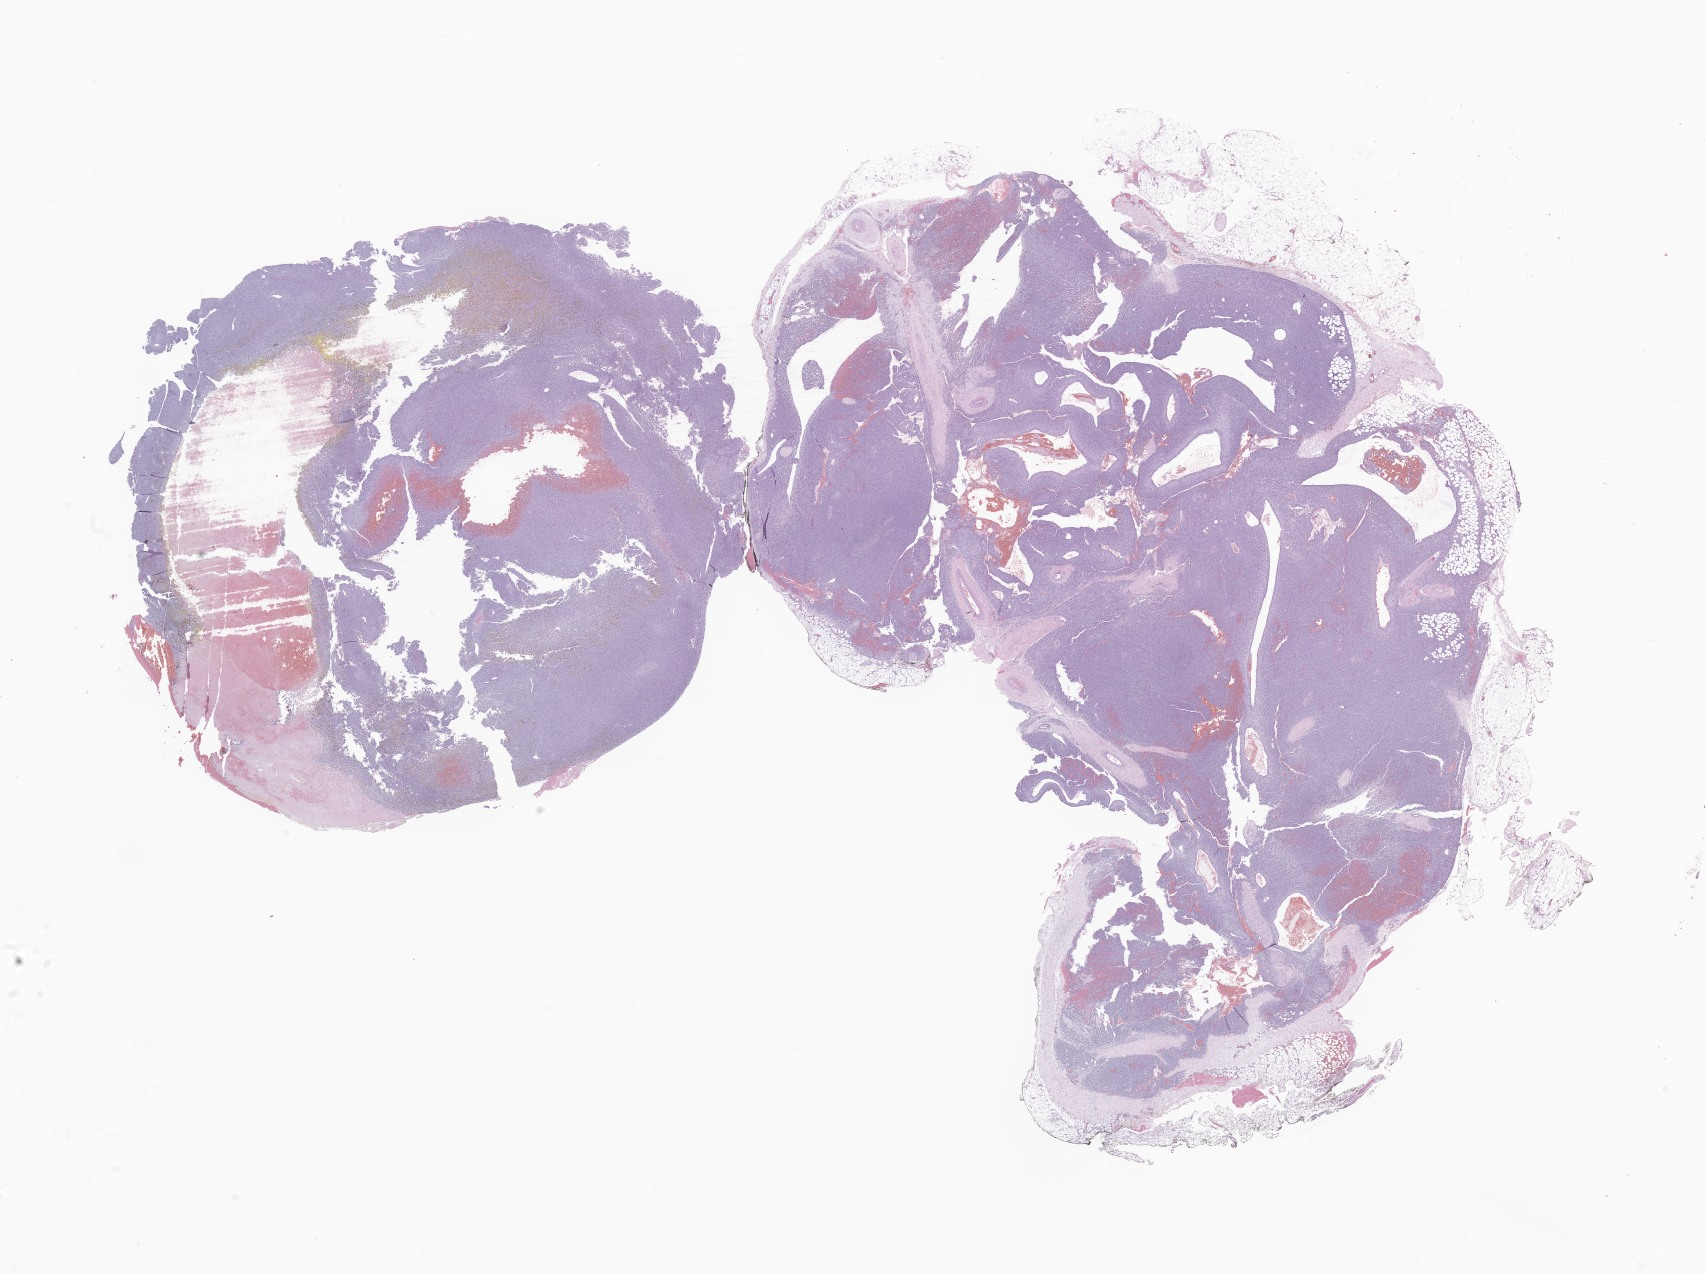
Hematoxylin and eosin (H&E) whole-slide image of tumor tissue from the soft tissue of upper extremity, low-resolution overview of the scanned area, about 28.8 x 21.5 mm. Formalin-fixed, paraffin-embedded (FFPE) tissue. Patient female; age 209 days.
Diagnosis: Infantile fibrosarcoma.